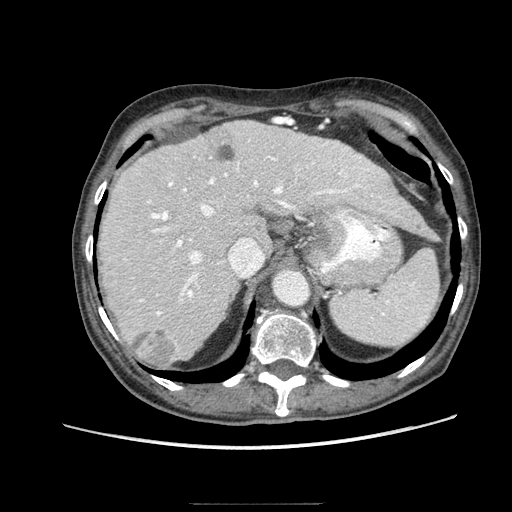
Contrast-enhanced abdominal CT (liver protocol), one axial slice. Position 61 of 83 along the scan axis. Reconstruction kernel STANDARD. 140 kVp. Soft-tissue window (W 400 / L 40 HU). 2.5 mm slice thickness. 512 × 512 image matrix, field of view 360 × 360 mm. Case-level facts recorded for this patient, not image findings: diagnosis: hepatocellular carcinoma (patient treated with transarterial chemoembolisation; whether this scan precedes or follows treatment is not stated here); TNM stage (as recorded): Stage-I; Child-Pugh class: A; tumour differentiation: moderately differentiated; tumour nodularity: uninodular.
Outlined on this slice (semi-automatically segmented with operator editing):
- abdominal aorta: bounding box [x1, y1, x2, y2] px = [274, 271, 309, 305]
- liver parenchyma outside the tumour (the mass and vessels are separate outlines, so this box may not span the whole liver): [98, 120, 422, 366]
- mass: [131, 326, 178, 367]
- liver vessels: [125, 140, 381, 316]